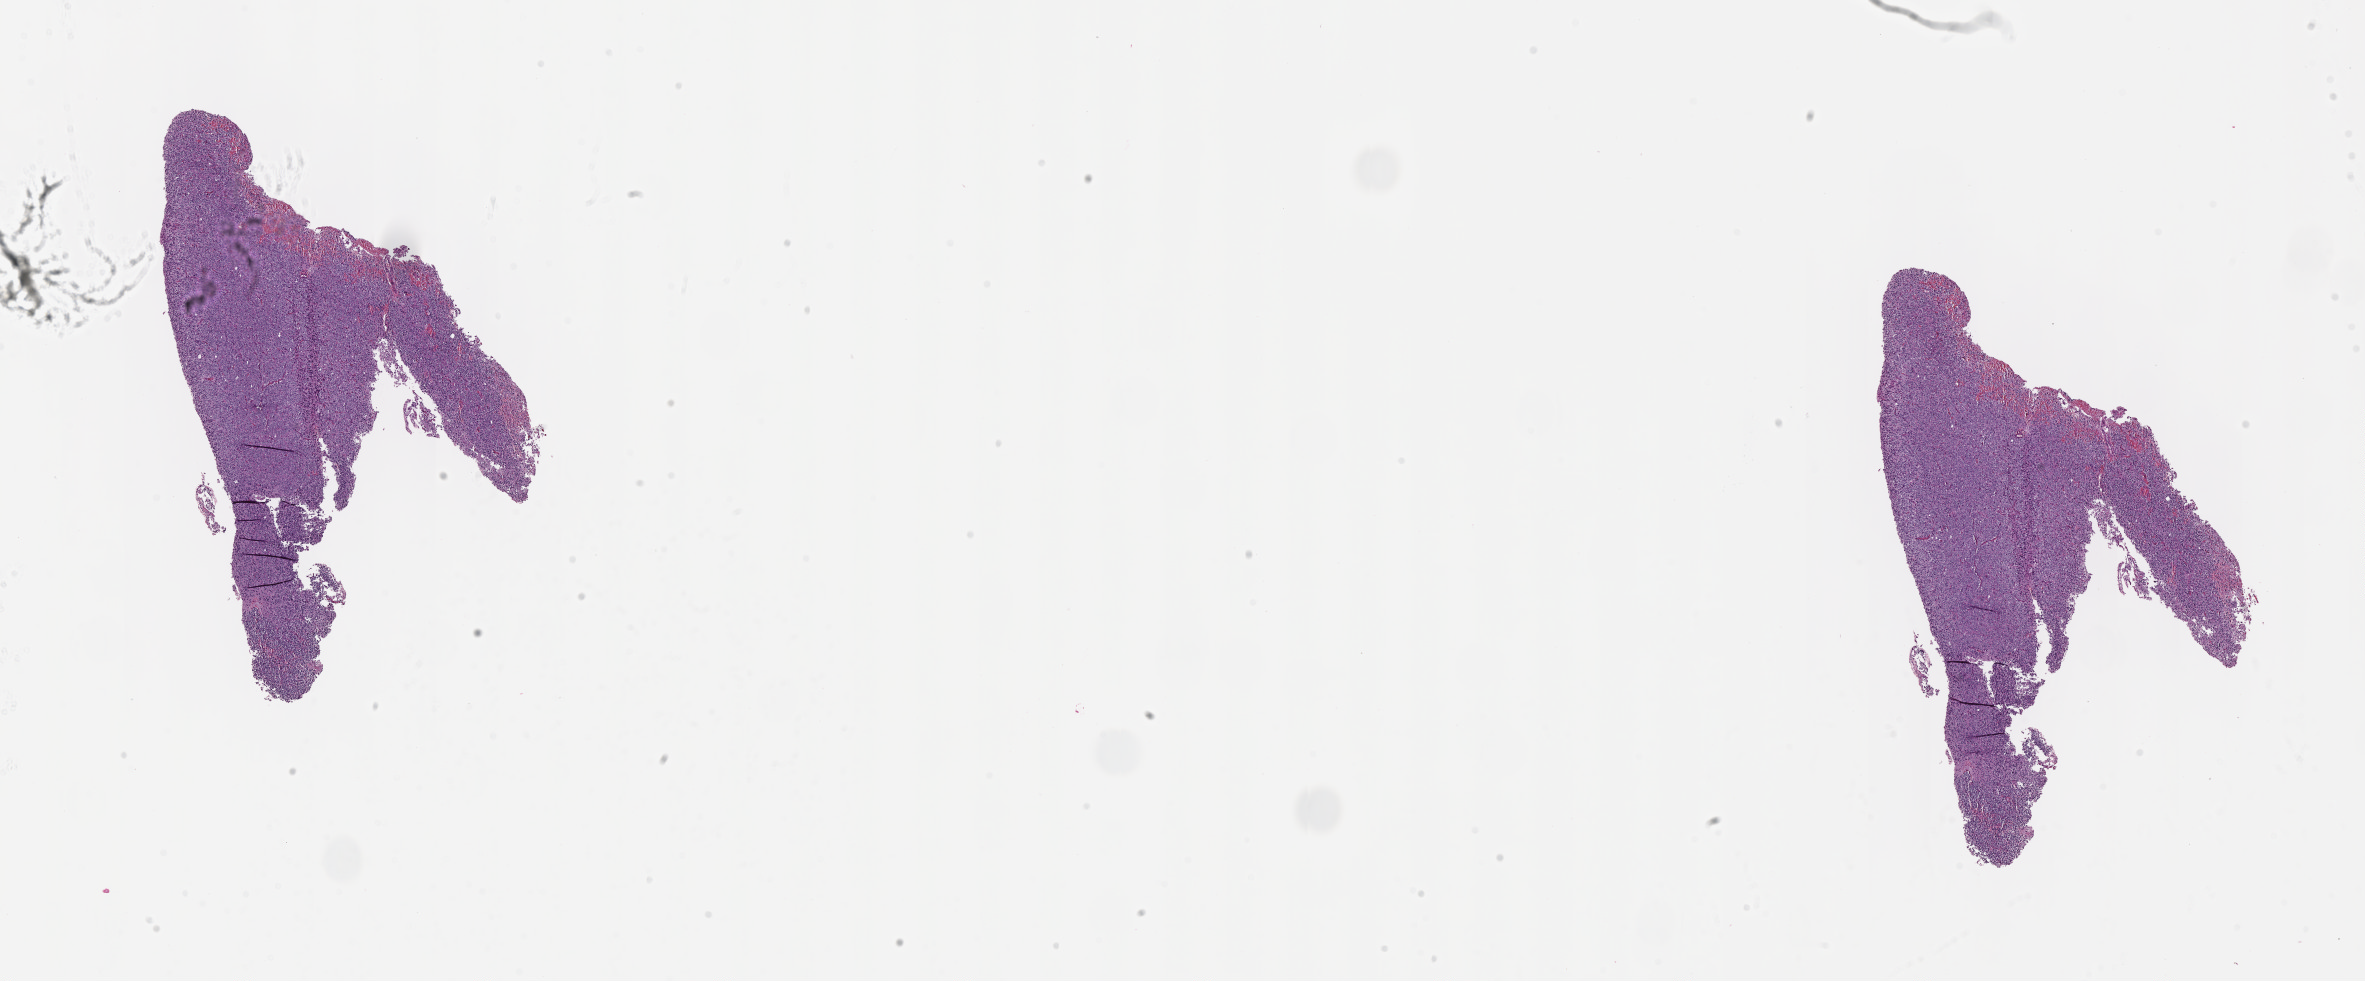
Digitized H&E-stained tissue section (whole slide) — whole scanned area (about 19.1 x 7.9 mm, acquisition: 40x scan) shown as a low-resolution overview, FFPE section, sample: primary tumour, brain. Patient: male, age at initial diagnosis 60 years. Histologic grade: G2 (moderately differentiated).
• histologic diagnosis: Oligodendroglioma, NOS (cerebrum)
• laterality: right